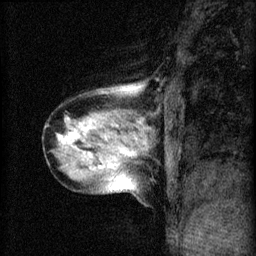
Breast MRI (dynamic contrast-enhanced), one sagittal slice; slice 21 of 60 in the series (ordered by position); 3 images stored at this slice position (order not interpretable as contrast timing); 1.5 T; TE 4.2 ms, TR 8.2 ms; 2 mm slice thickness; 256 × 256 image matrix, field of view 180 × 180 mm. Female patient, age 40 years.
Annotated regions visible in this slice (semi-automatic segmentation, software-assisted and operator-edited):
- analysis volume of interest (the breast-tissue region the enhancement analysis was run in; not a lesion): bounding box (x1, y1, x2, y2) in pixels: (42, 80, 166, 195)
- tumour enhancement mask (voxels above the 70 % enhancement threshold inside the analysis volume of interest): (60, 126, 138, 169)